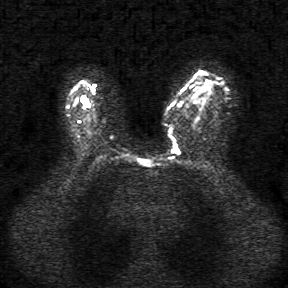
Breast MRI, one axial slice; position 24 of 34 along the scan axis; diffusion-weighted series; image 2 of 4 stored at this slice position (different b-values; order by instance number); 1.5 T; 5 mm slice thickness; 288 × 288 image matrix, field of view 340 × 340 mm. Female patient.
Annotated regions visible in this slice (expert manual segmentation):
- tumour on diffusion-weighted imaging: box from (x=82, y=98) to (x=90, y=107) px